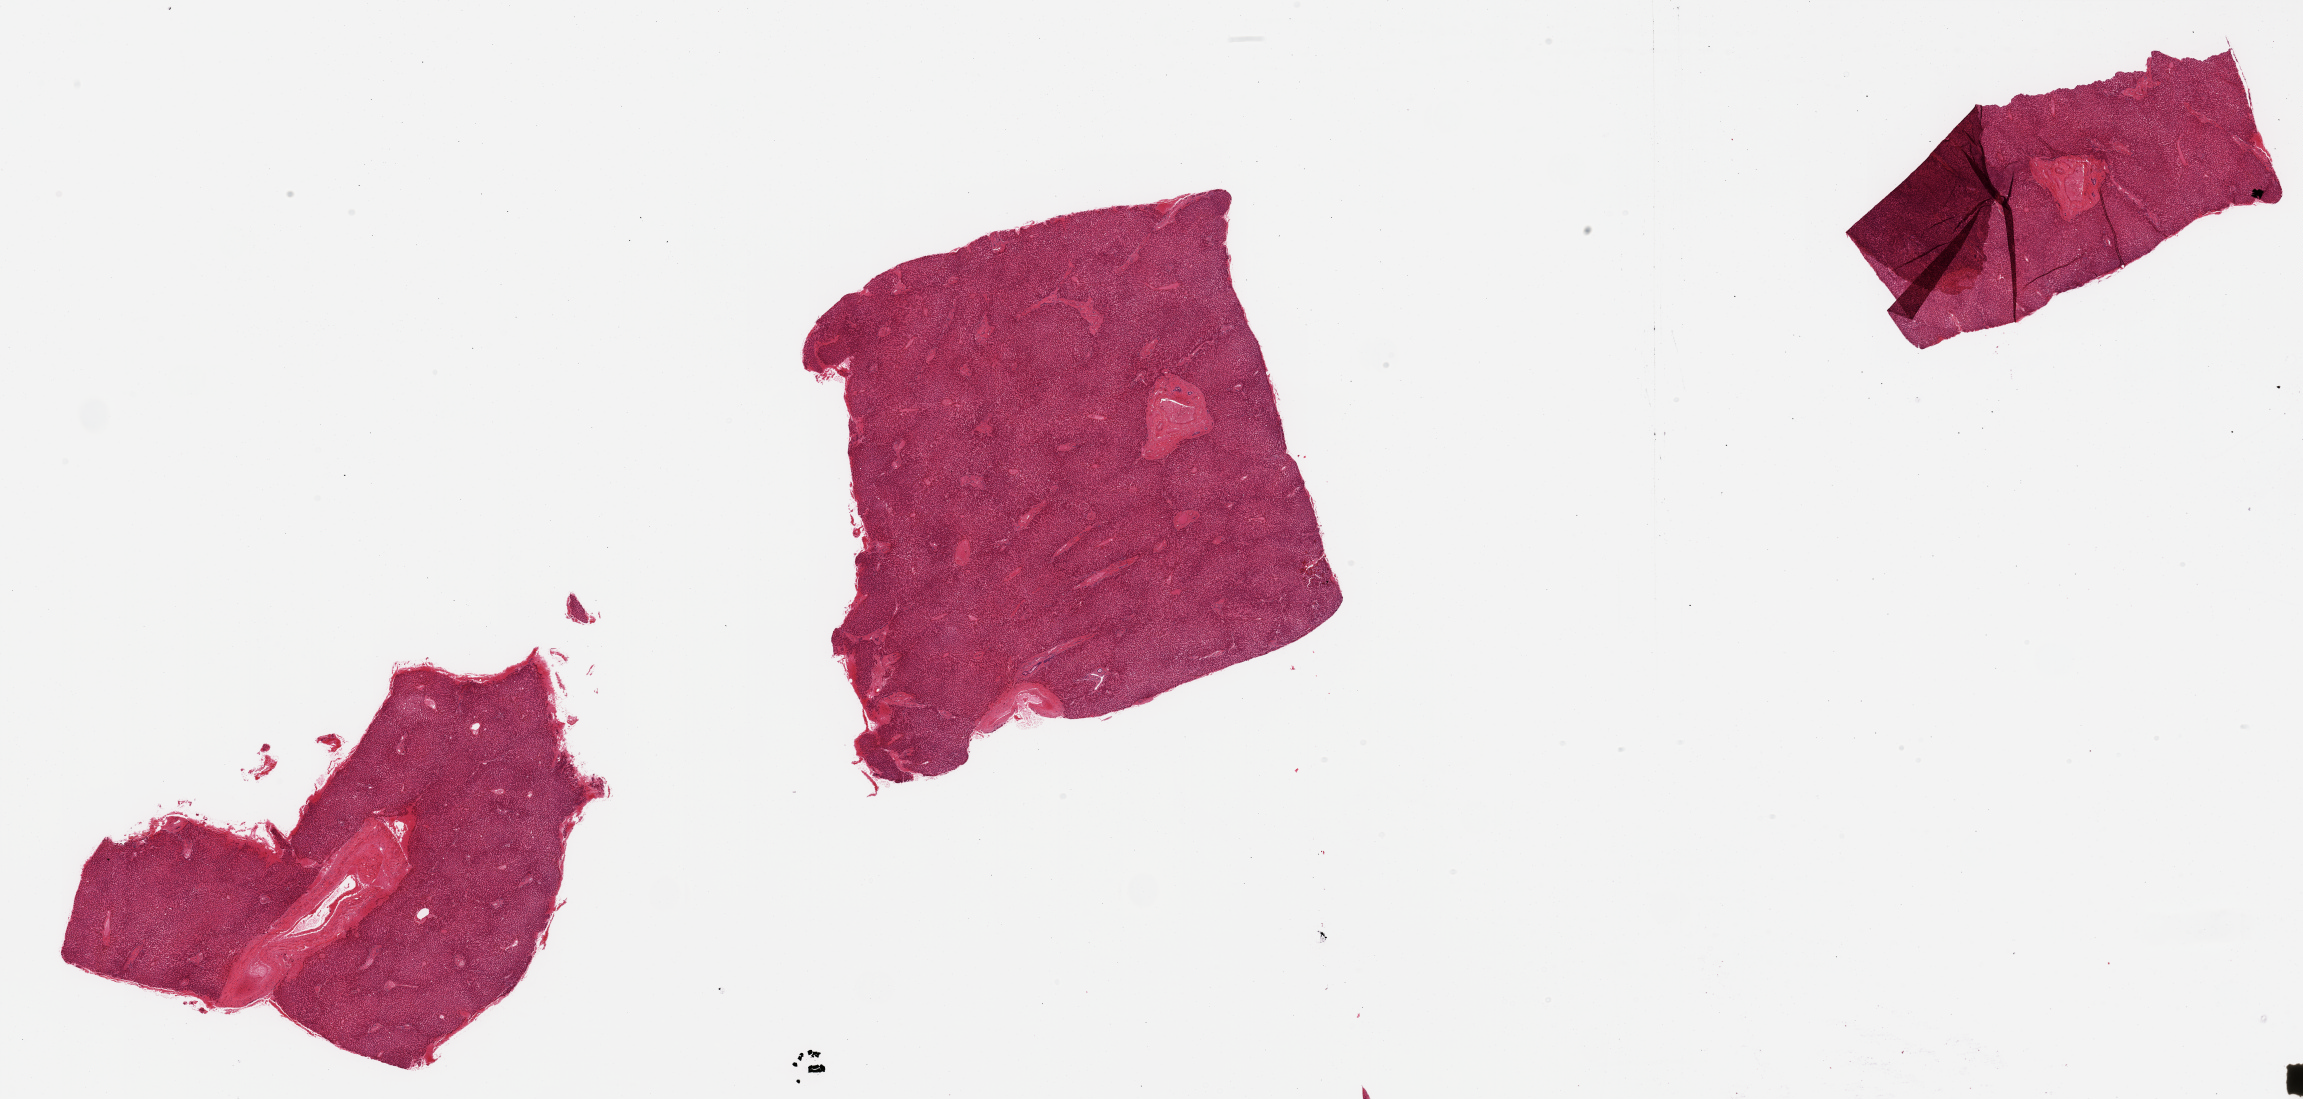
Haematoxylin and eosin whole-slide image, brightfield, shown as a low-resolution overview of the whole scanned area (about 36.4 x 17.4 mm), PAXgene-fixed, paraffin-embedded tissue, section of liver (target tissue), tissue donor sample. Donor sex: female.
Pathologist's review note for this sample: 3 pieces; accentuation of portal tracts with fibrosis and congestion.